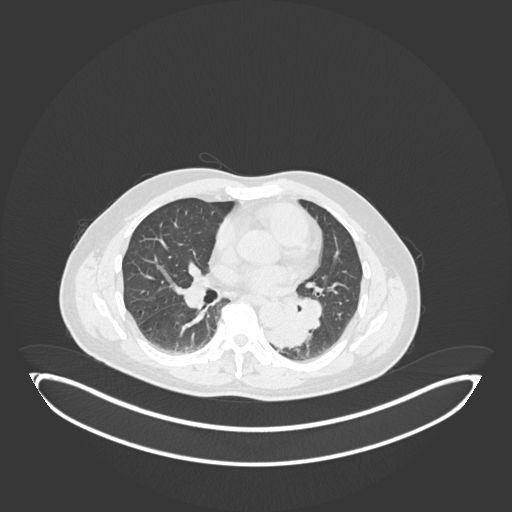
Chest CT, one axial slice. Slice 98 of 258 in the series (ordered by position). Reconstruction kernel B30f. 120 kVp. Lung window (W 1500 / L -600 HU). 1 mm slice thickness. 512 × 512 image matrix, field of view 500 × 500 mm. Male patient, age 54 years. Case-level facts recorded for this patient, not image findings: clinical TNM (as recorded): T3 N0 M0.
Annotated regions visible in this slice (bounding box drawn by a radiologist):
- lung tumour (recorded histology: squamous cell carcinoma): bounding box [x1, y1, x2, y2] px = [267, 300, 315, 352]